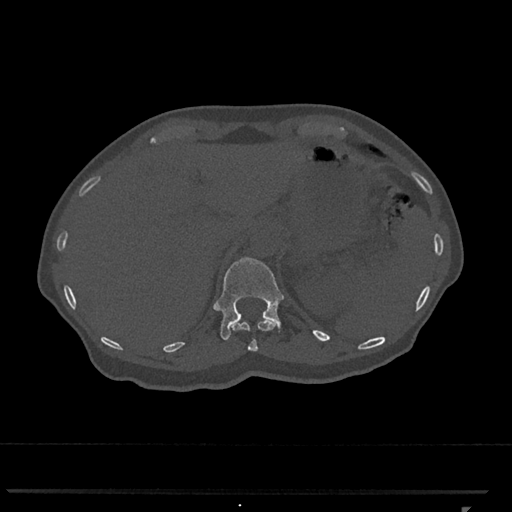
CT including the spine, one axial slice; slice 483 of 793 in the series (ordered by position); reconstruction kernel Br40s/3; 120 kVp; bone window (W 1800 / L 400 HU); 0.5 mm slice thickness; 512 × 512 image matrix, field of view 380 × 380 mm. Patient: female, 62 years. From the clinical record (not read from this slice): primary cancer: renal.
Outlined on this slice (semi-automatic segmentation, software-assisted and operator-edited):
- T11 vertebra: bounding box (x1, y1, x2, y2) in pixels: (232, 319, 275, 351)
- T12 vertebra: (214, 257, 284, 340)